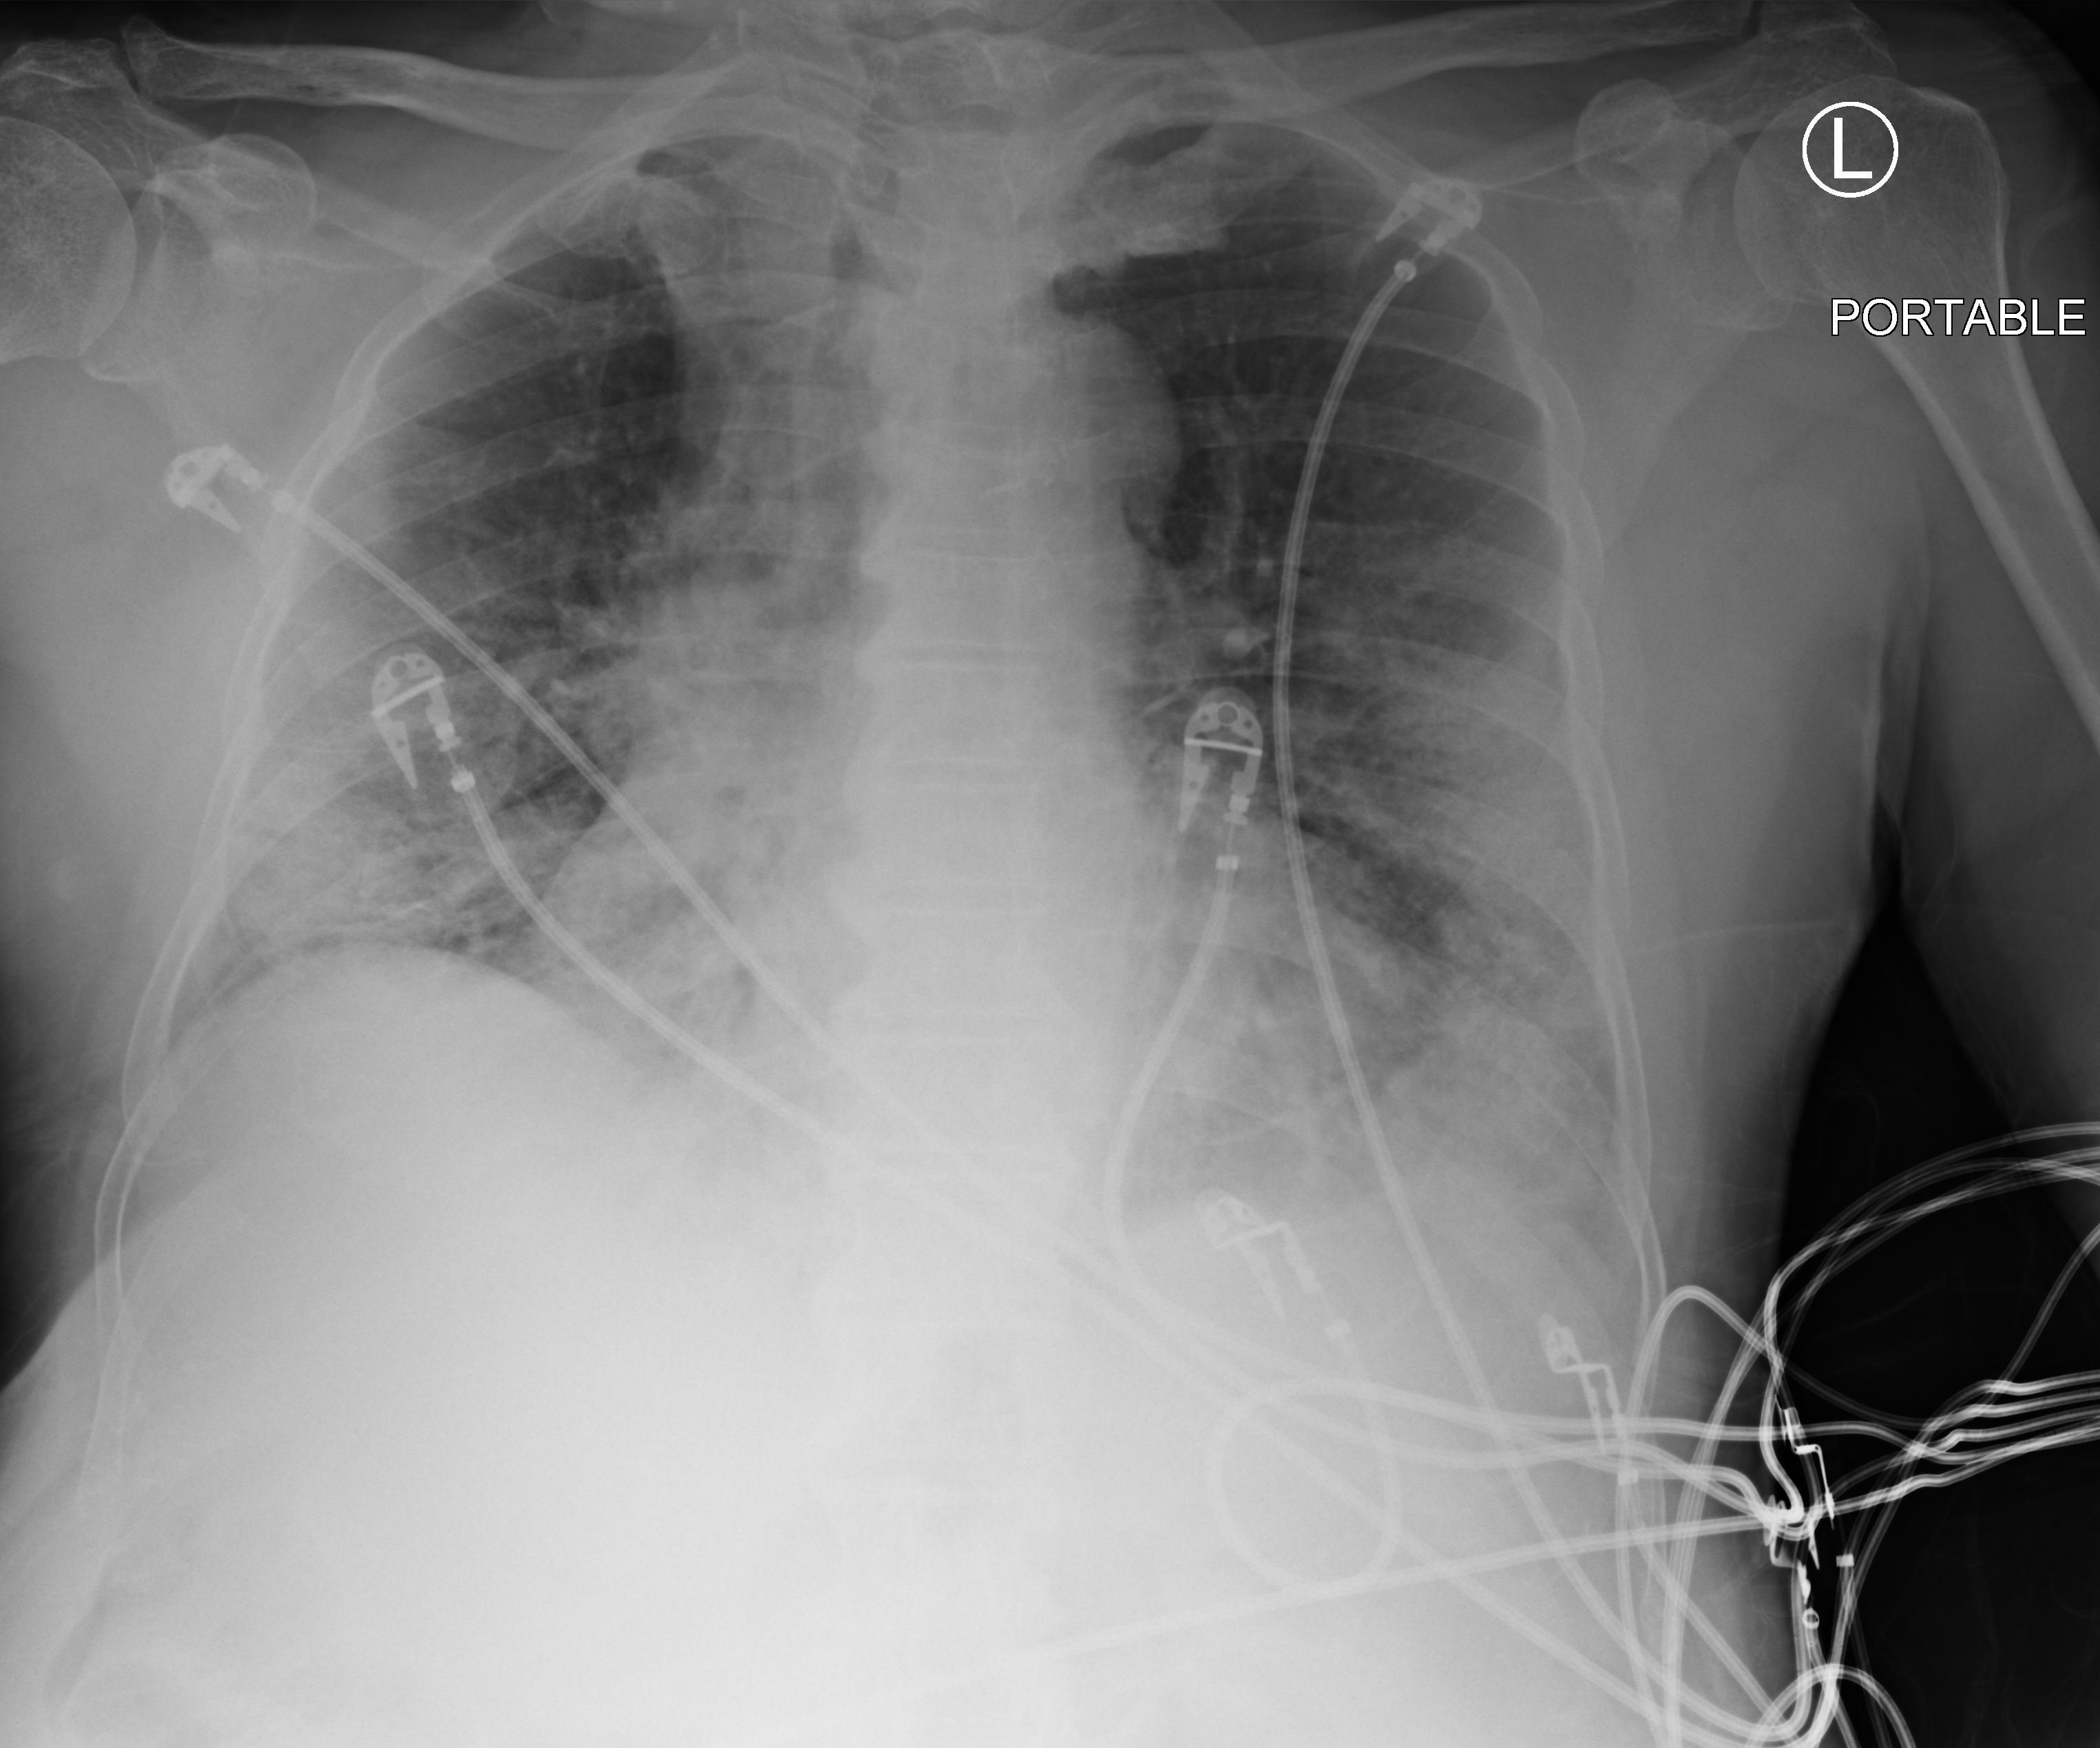
Chest X-ray (portable). Male patient hospitalised with COVID-19, age 60–74 years.
Admission-level facts for this patient (not findings on this image; timing relative to this image not recorded):
- smoking status (admission record): never
- mechanically ventilated during this hospital stay: yes
- admitted to intensive care during this hospital stay: yes